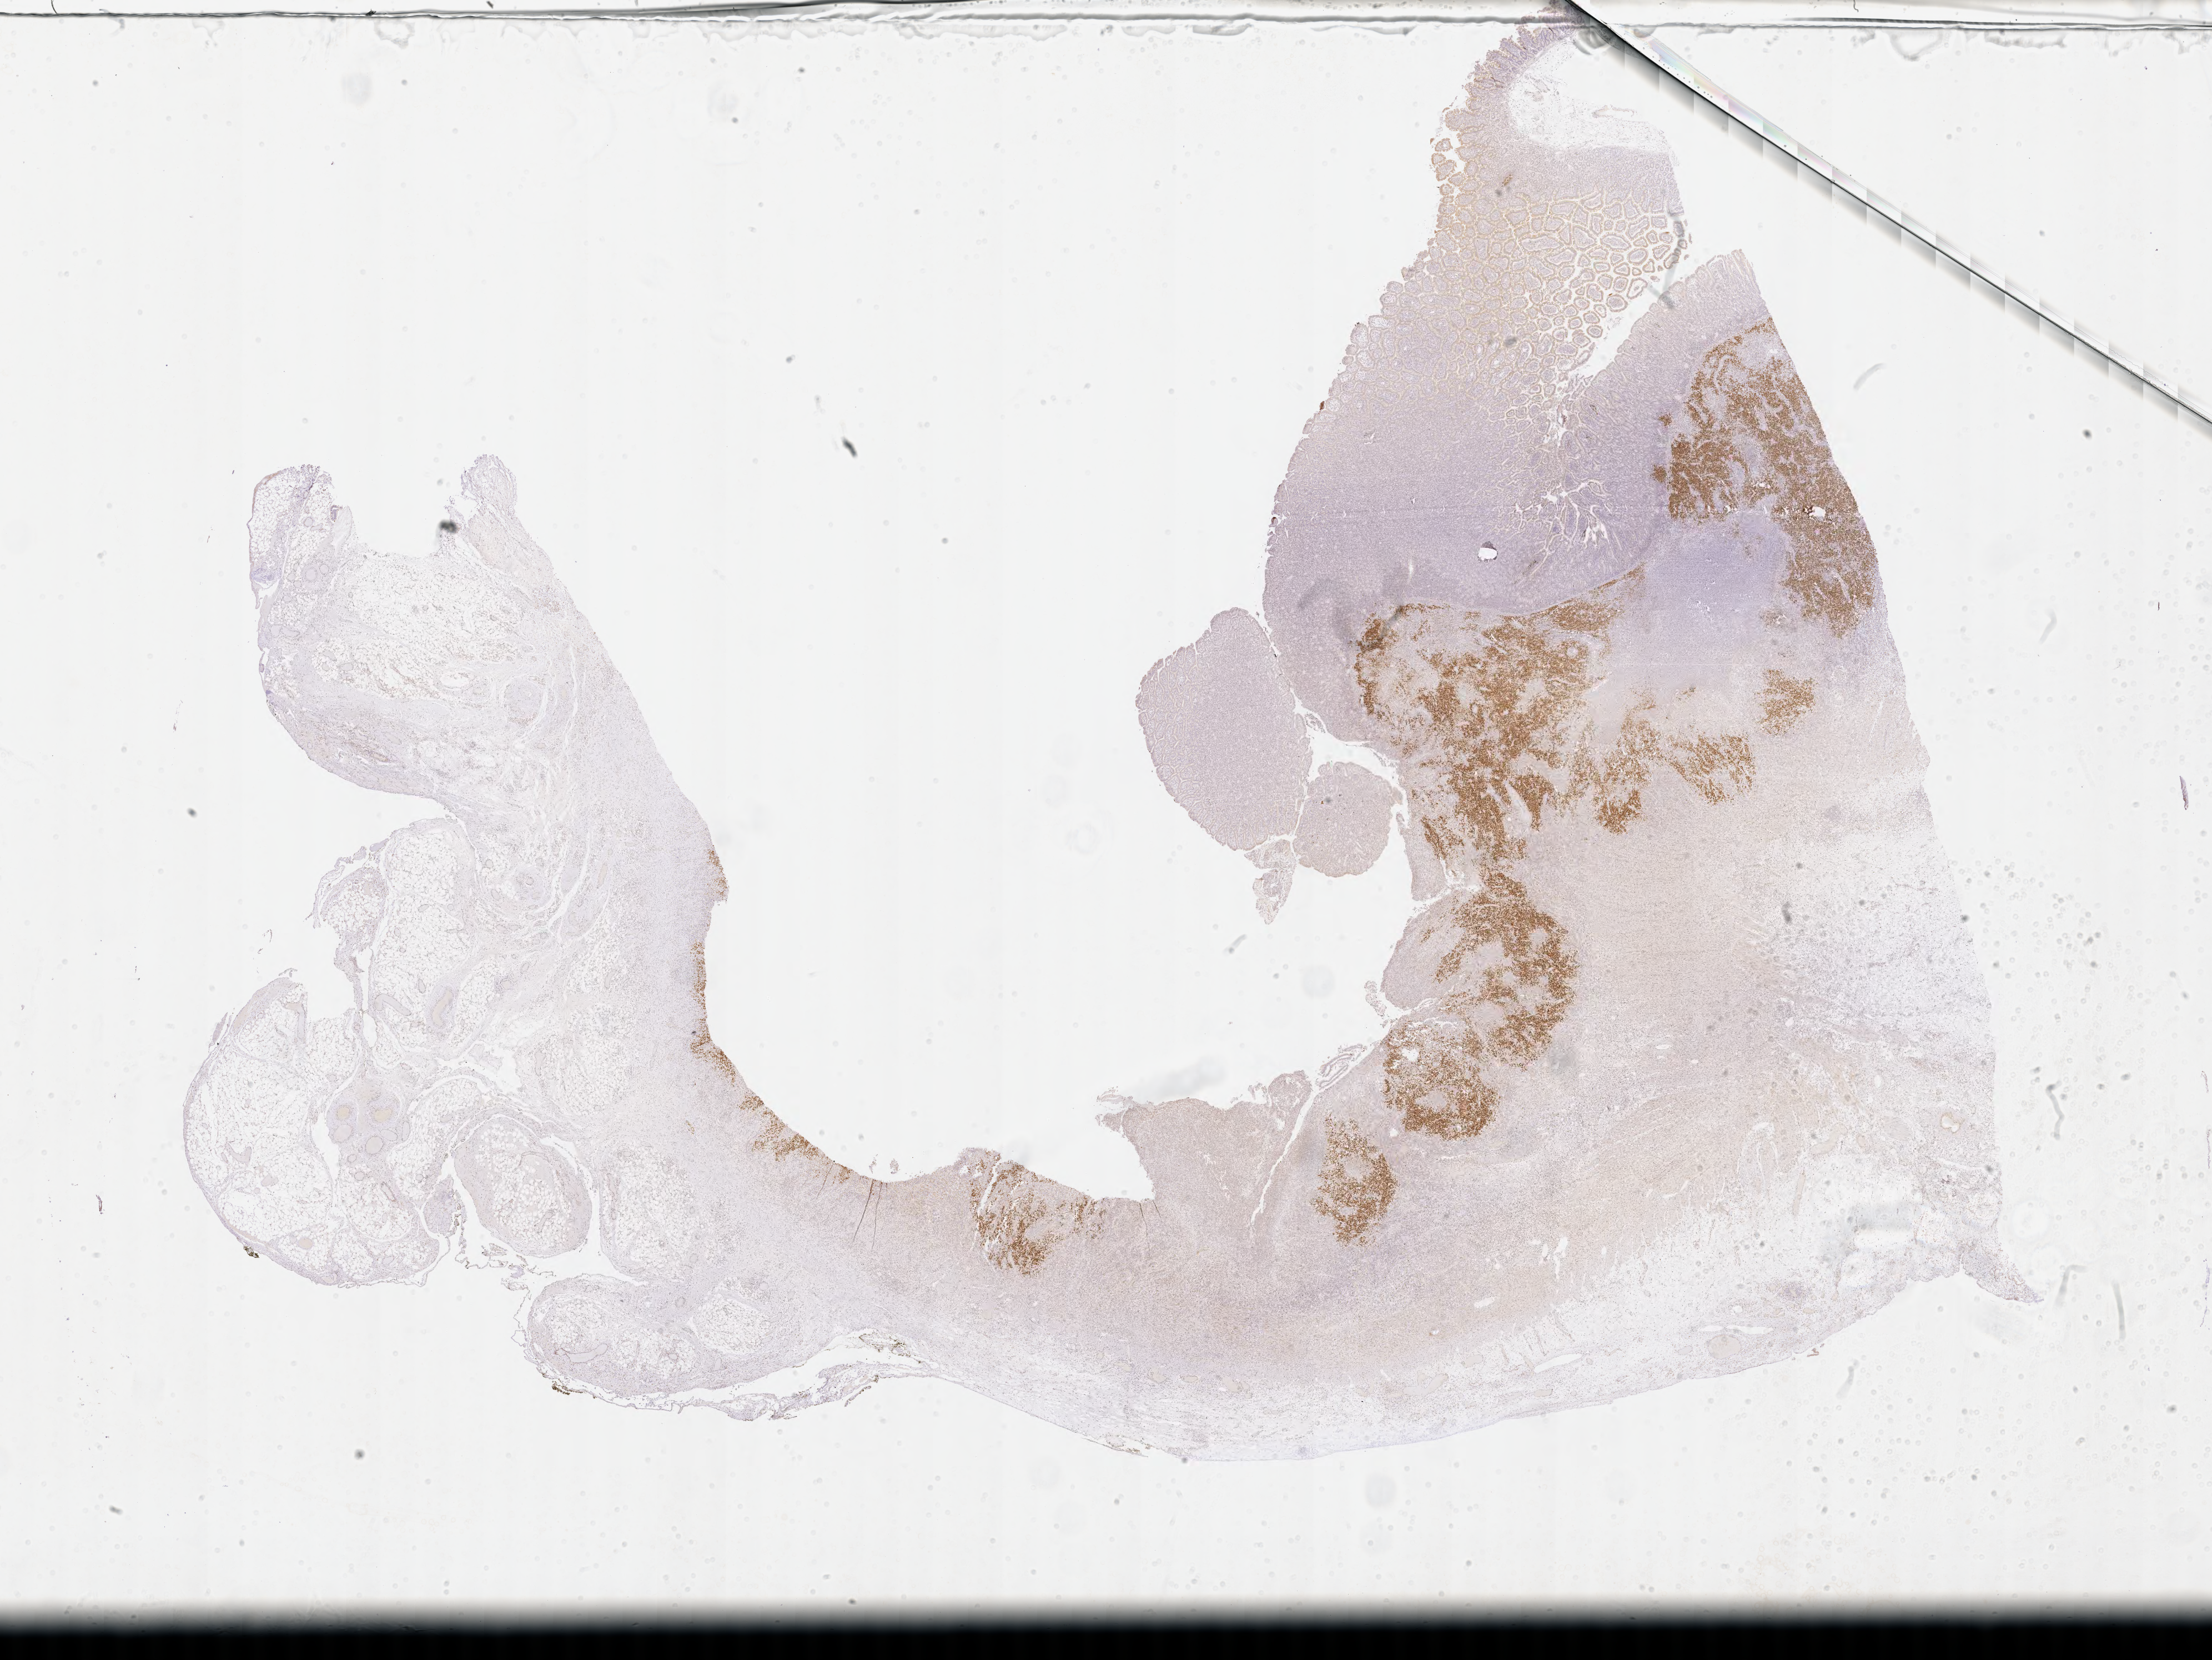
IHC for BCL6, whole-slide image, whole scanned area (about 32.2 x 24.2 mm) shown as a low-resolution overview. Specimen: tumor tissue. Patient female; age 44 years.
Diagnosis: Burkitt lymphoma, NOS.